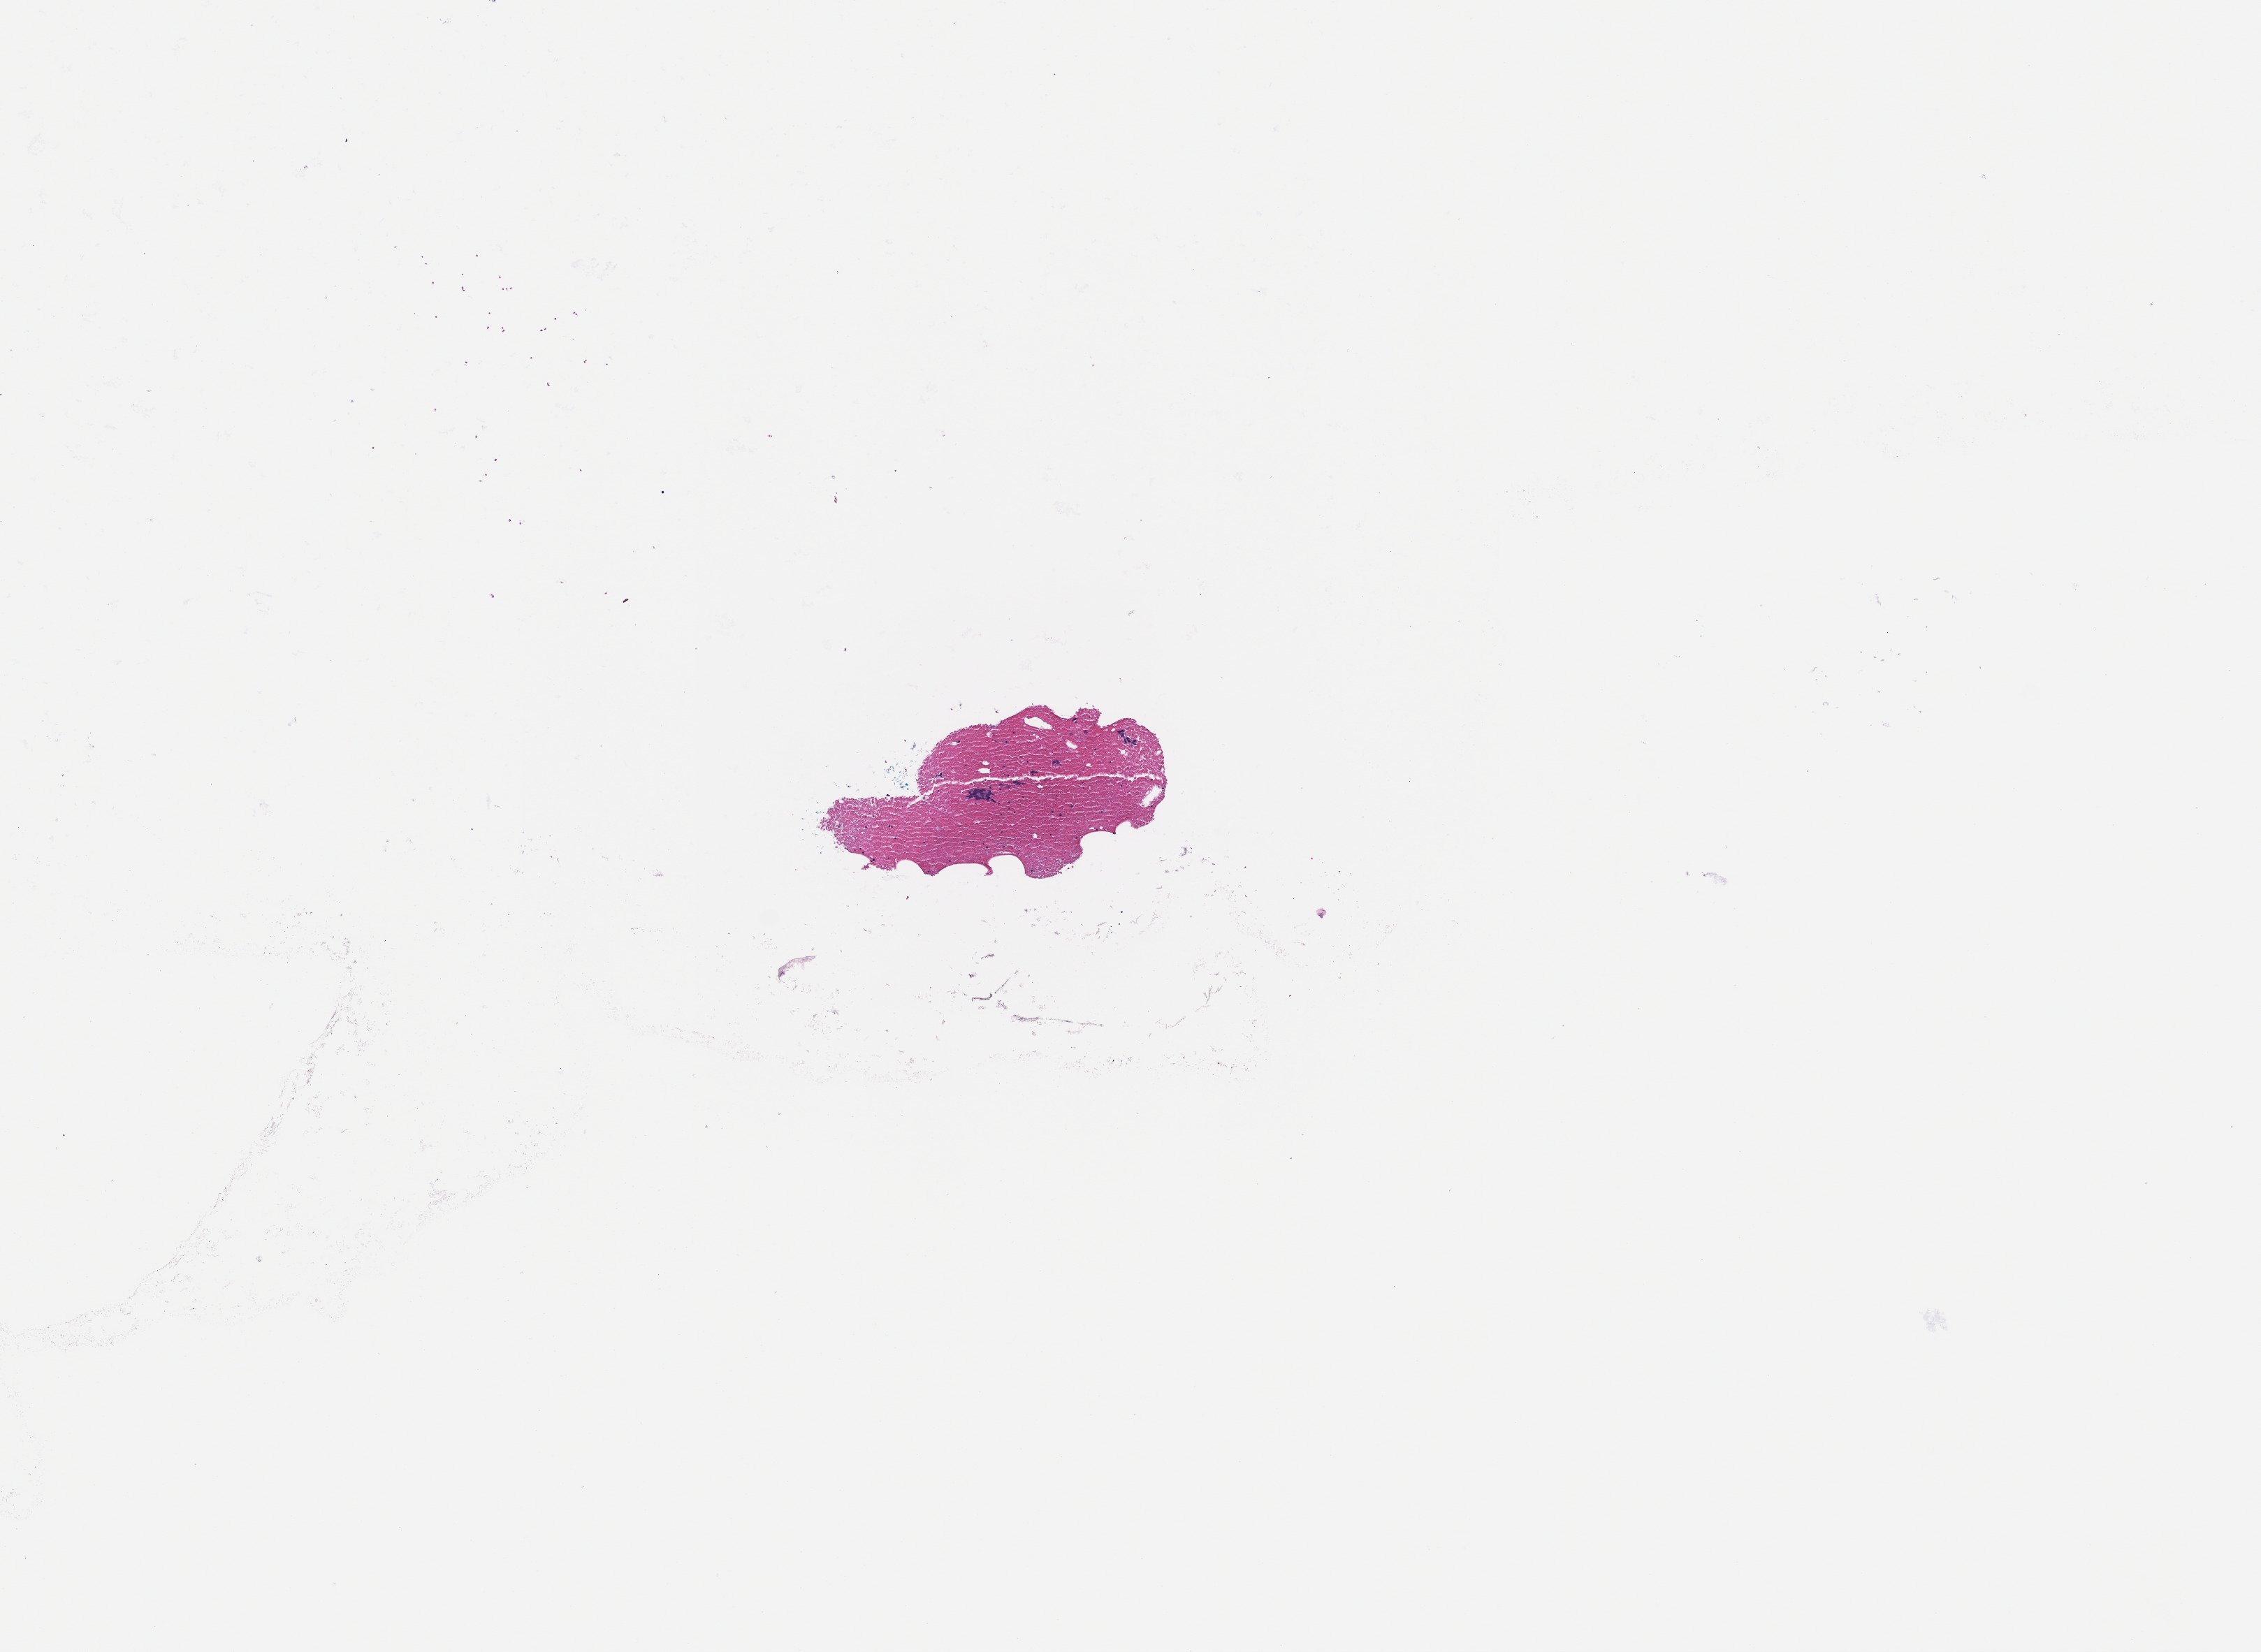
Haematoxylin and eosin whole-slide image, shown as a low-resolution overview of the whole scanned area (about 6.5 x 4.8 mm); formalin-fixed, paraffin-embedded (FFPE) tissue. Female patient.
- this section: metastasis (sampled organ not recorded)
- patient diagnosis (primary): Non-Small Cell Lung Carcinoma